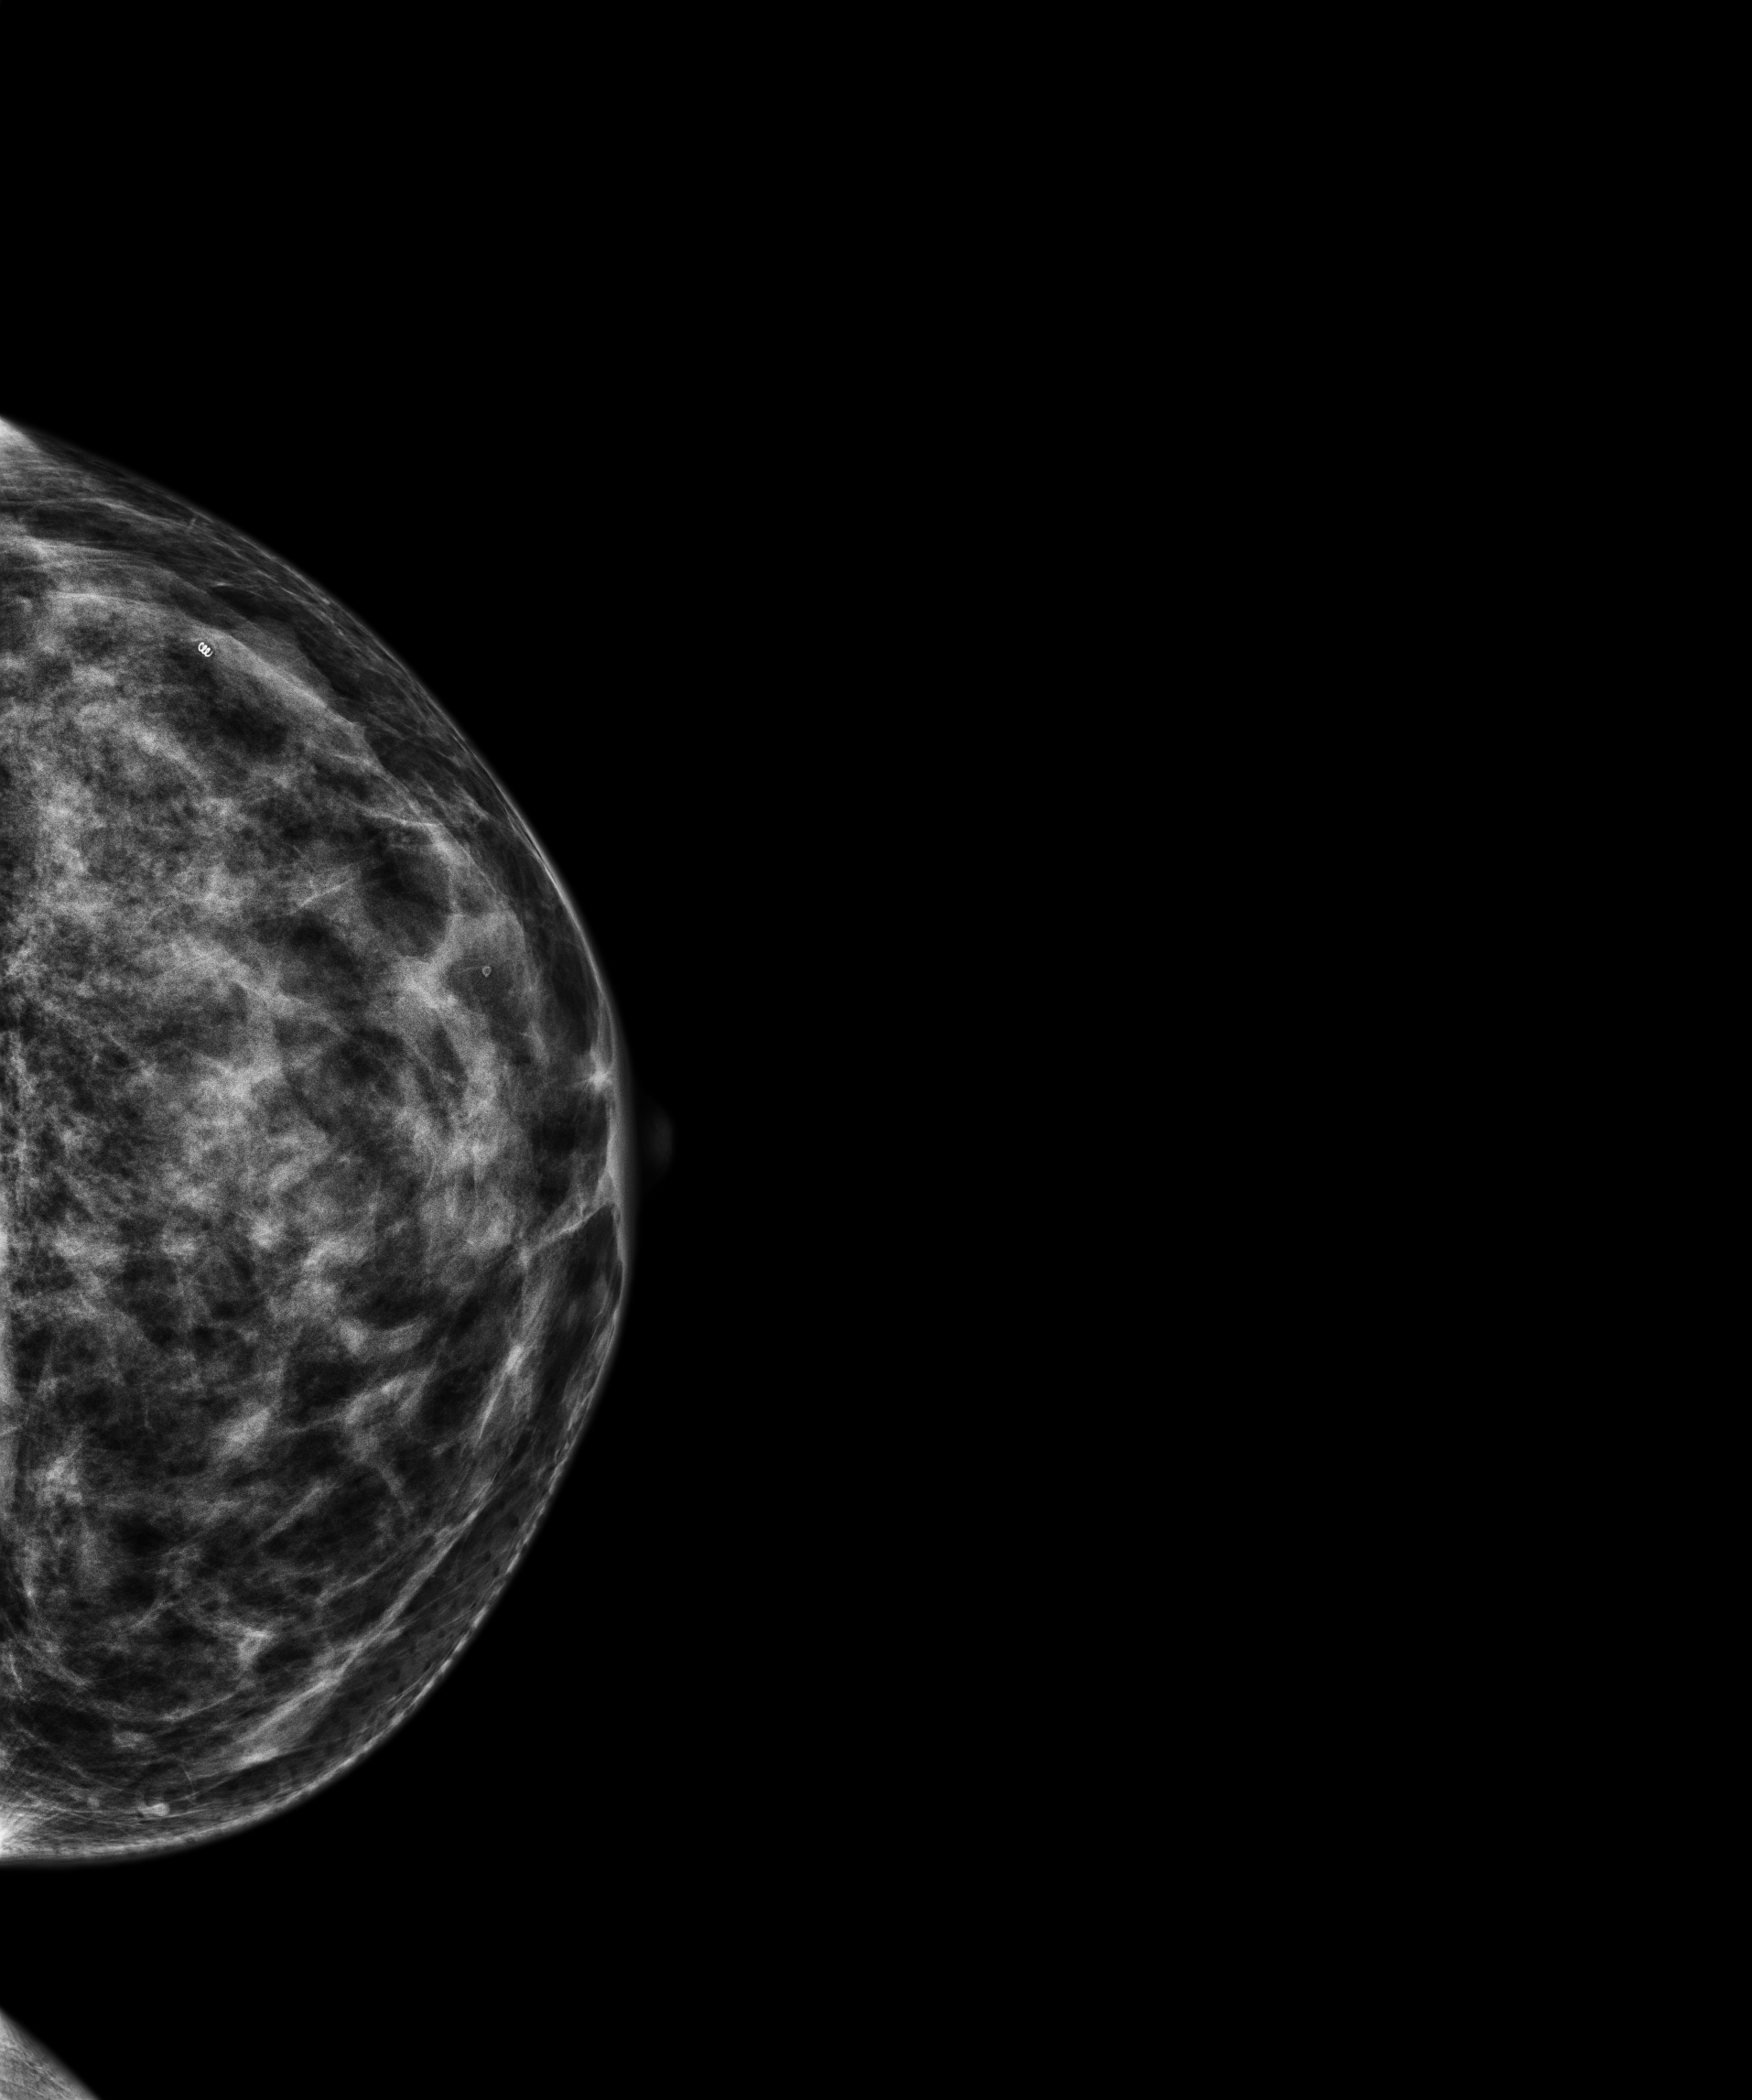
Annual screening mammography examination, compressed breast thickness 54.1 mm, system: Senographe Pristina. Patient aged 44 years (female).
Image type: full-field digital mammogram. Breast: left. Projection: cranio-caudal projection.